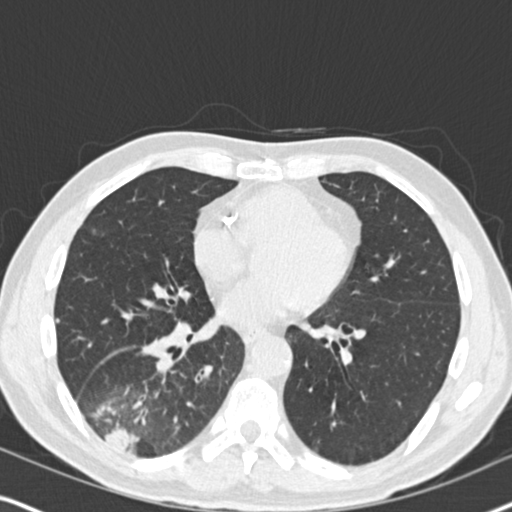
Low-dose screening chest CT, one axial slice; slice 86 of 182 in the series (ordered by position); reconstruction kernel B30f; 120 kVp; lung window (W 1500 / L -600 HU); 2 mm slice thickness; 512 × 512 image matrix, field of view 330 × 330 mm.
Annotated regions visible in this slice (expert manual segmentation):
- lesion 1 (tumor, lower lobe of right lung): bounding box (x1, y1, x2, y2) in pixels: (104, 426, 139, 451)